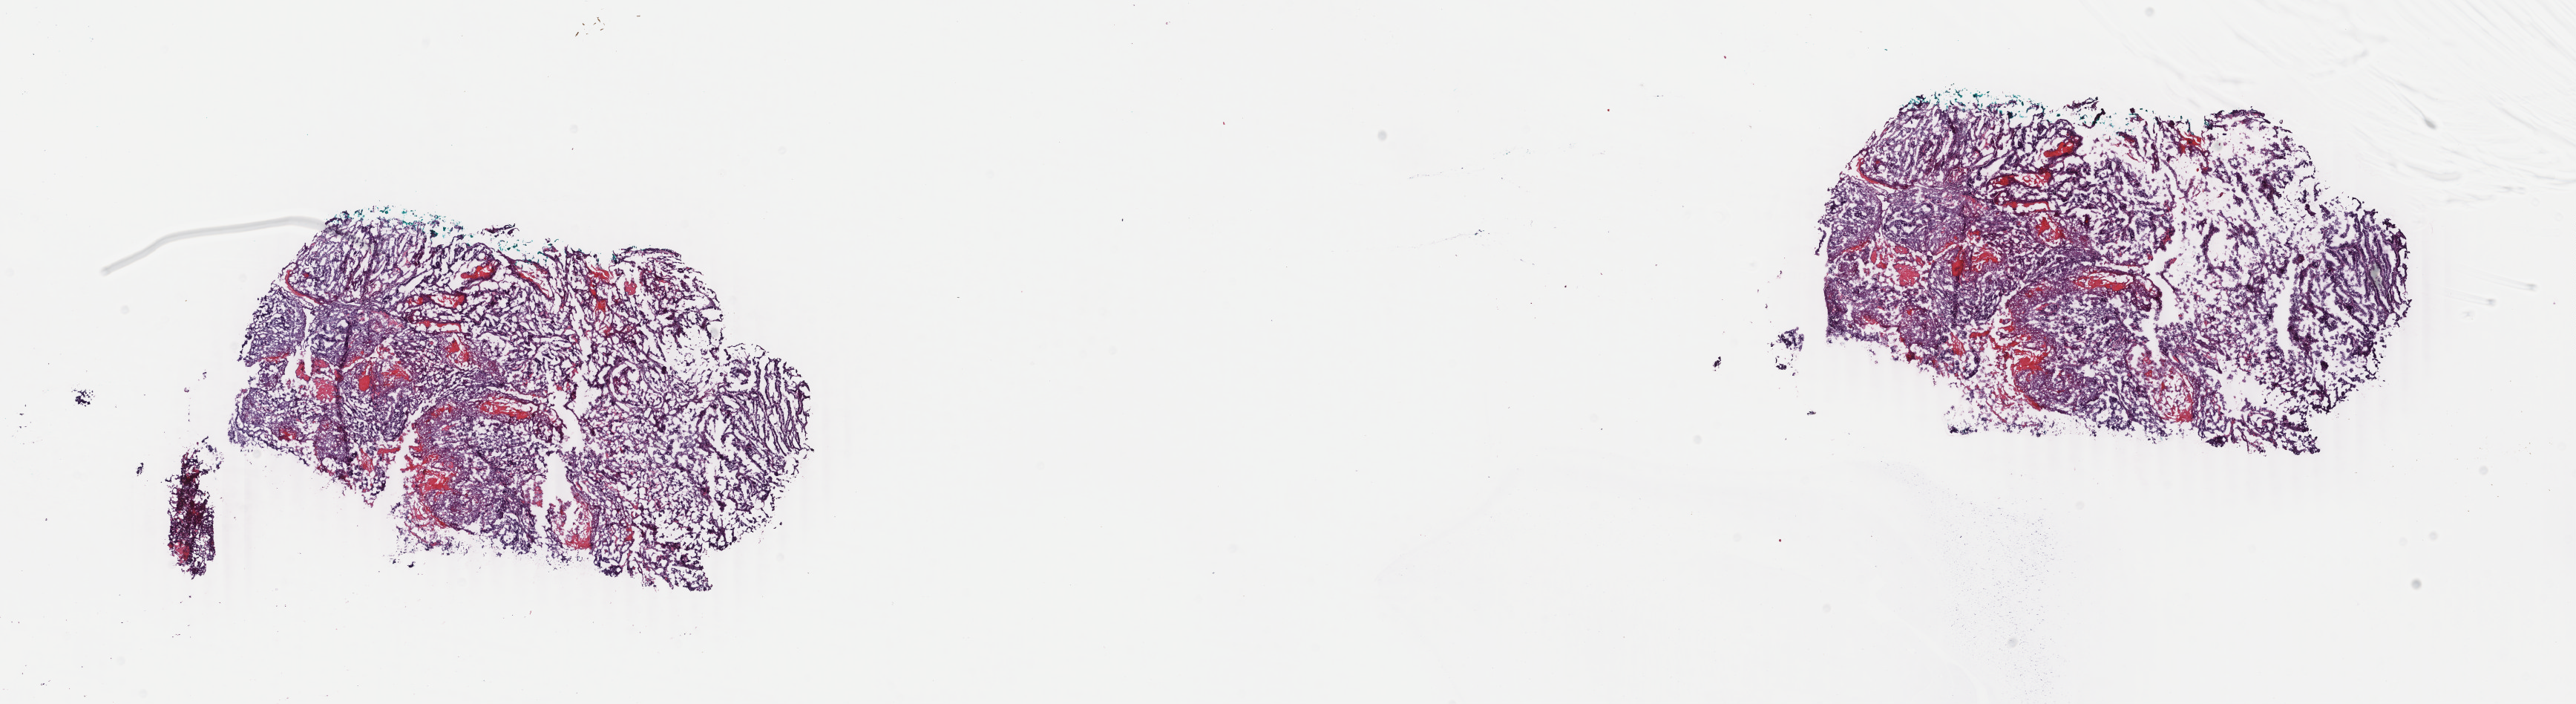
Digitized H&E tissue section (whole slide), low-resolution overview of the scanned area, about 27.6 x 7.5 mm (acquisition: 40x scan); frozen section from the top of the tissue portion; sample: primary tumour, uterus. Female patient; age at initial diagnosis 39 years.
Pathologic diagnosis: Endometrioid adenocarcinoma, NOS.